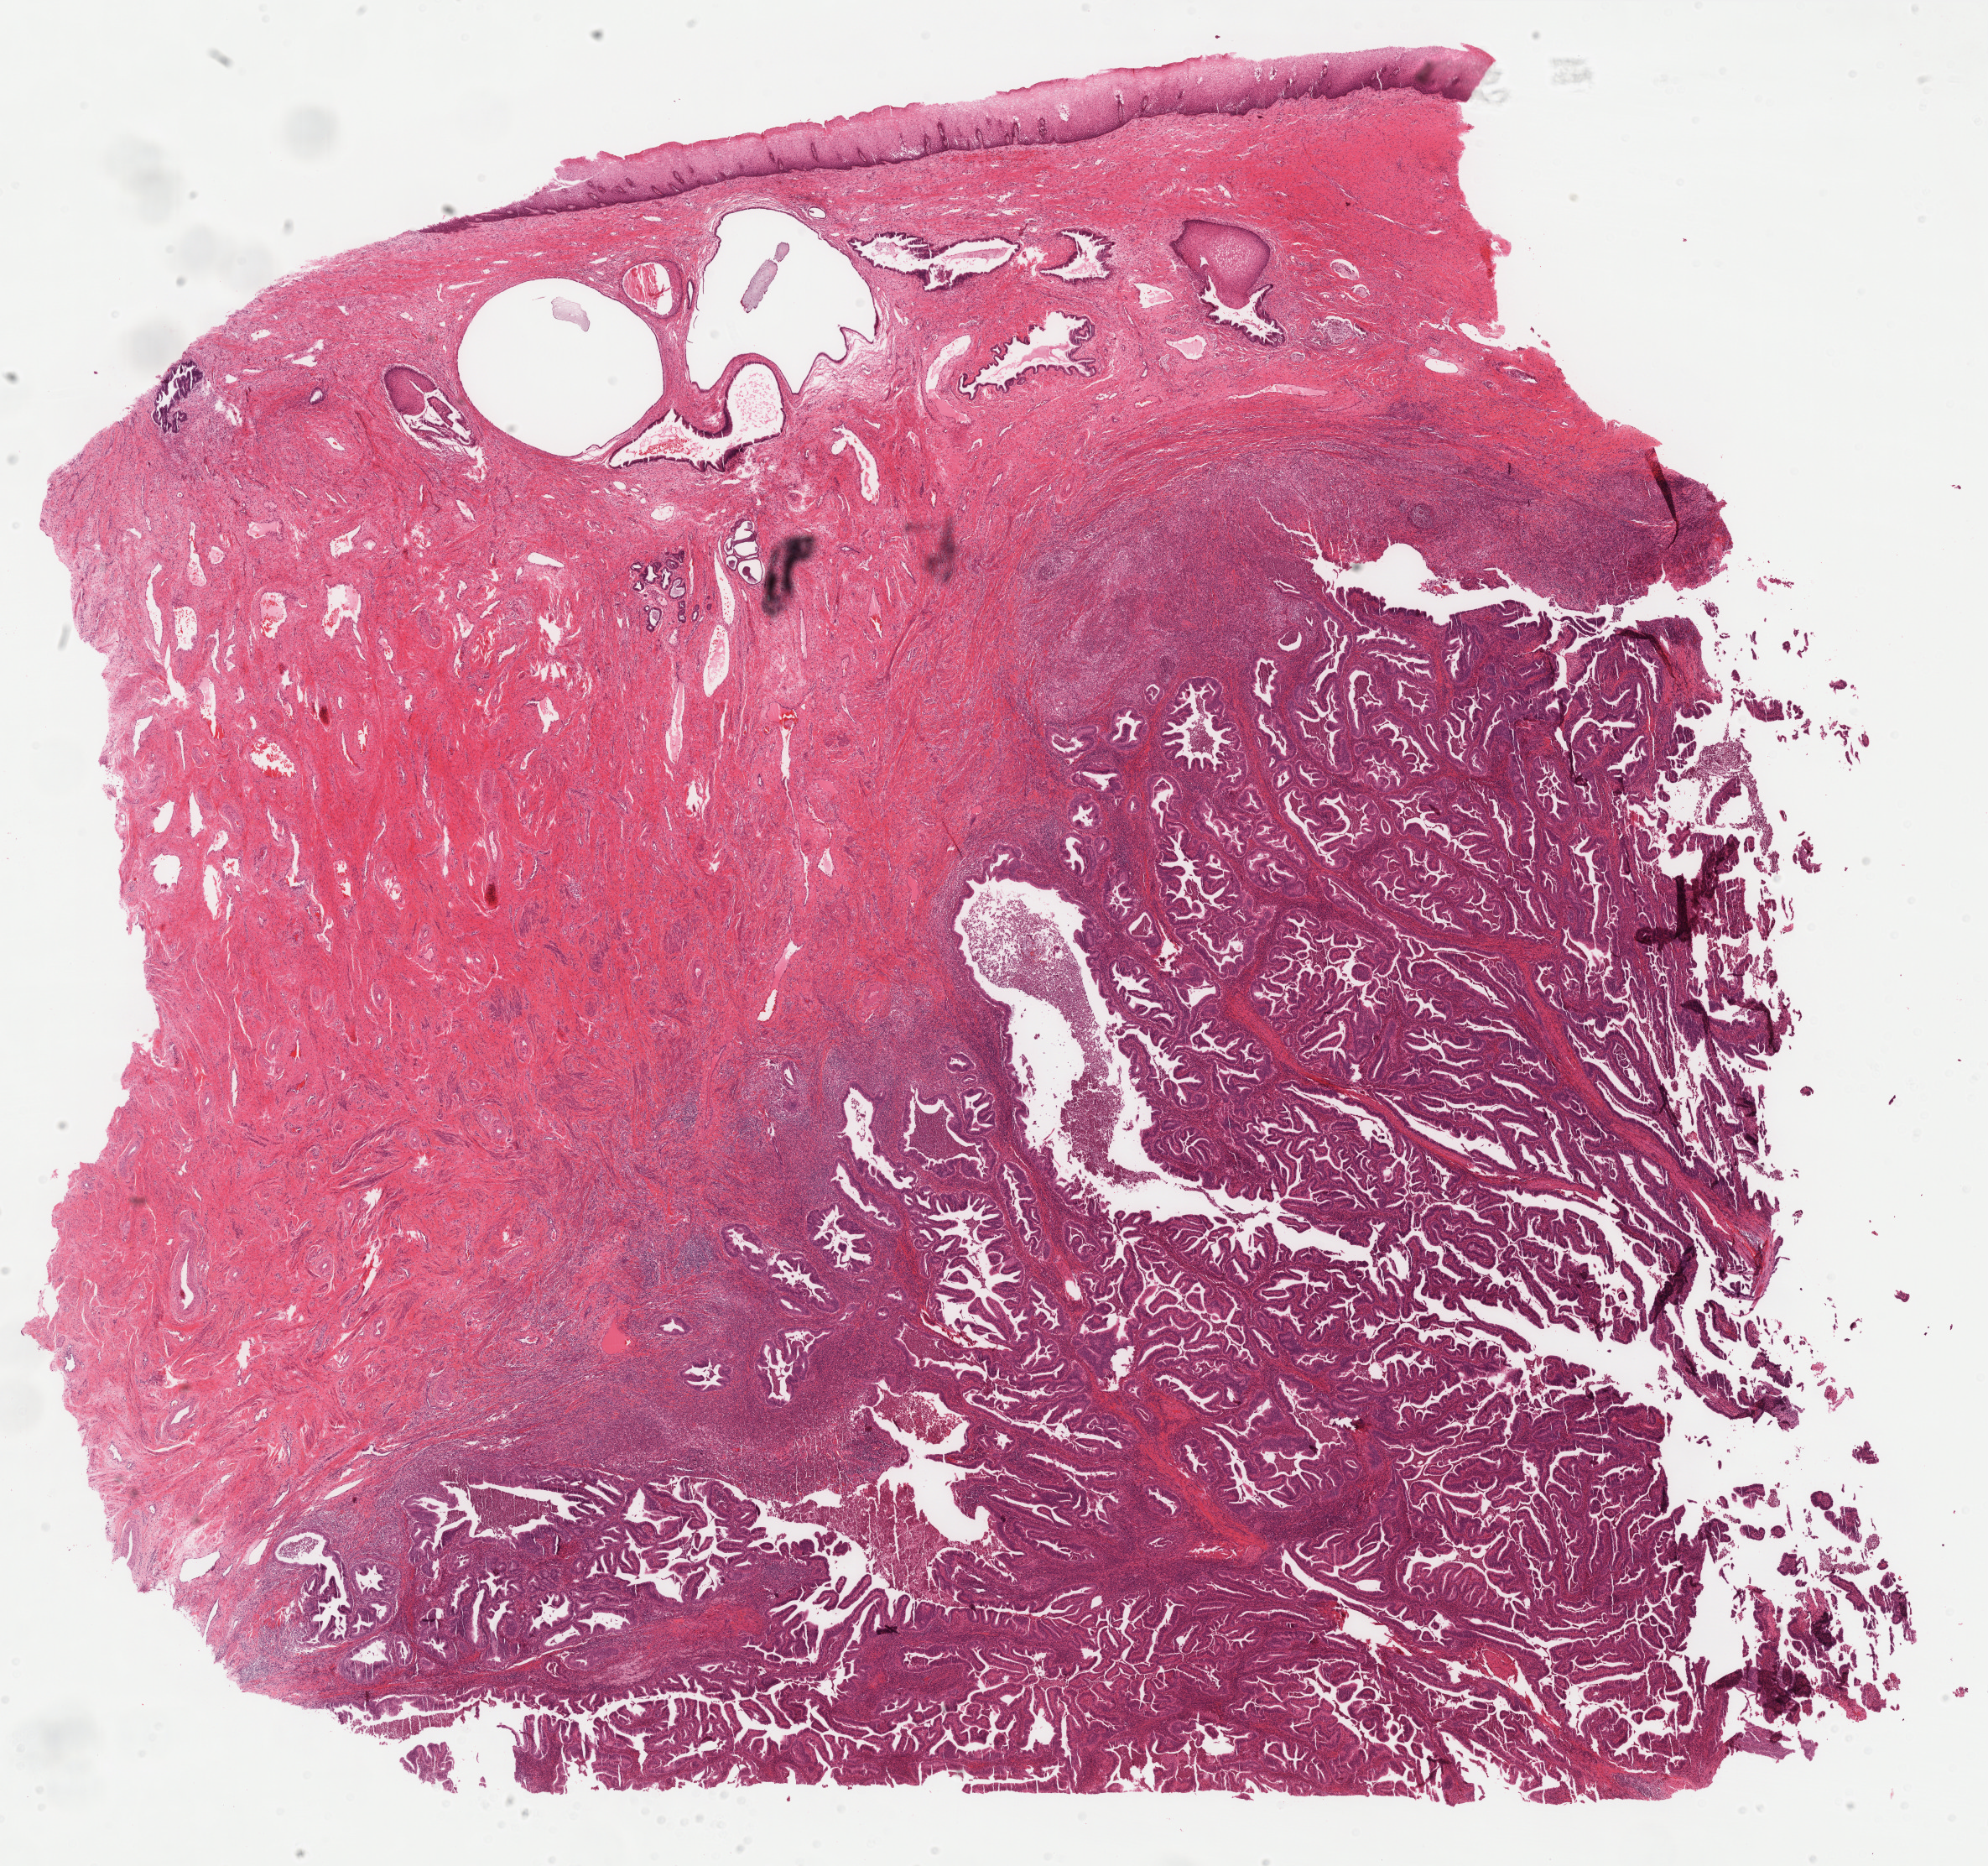
Whole-slide histology image, H&E — shown as a low-resolution overview of the whole scanned area (about 19.0 x 17.8 mm). FFPE section. Cervix, primary tumour sample. Patient: female, age at initial diagnosis 37 years. Histologic grade: G1 (well differentiated).
* diagnosis: Endometrioid adenocarcinoma, NOS (cervix uteri)
* lymph nodes positive (case pathology): 0 of 41 examined
* FIGO stage: IB2